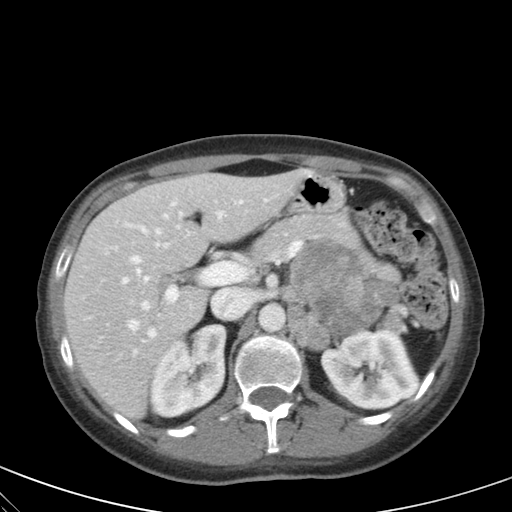
Contrast-enhanced abdominal CT, one axial slice. Position 35 of 59 along the scan axis. 120 kVp. Intravenous contrast given. Soft-tissue window (W 400 / L 40 HU). 4 mm slice thickness. 512 × 512 image matrix. Patient: female, 28 years. Case-level facts recorded for this patient, not image findings: diagnosis: adrenocortical carcinoma; tumour side: left adrenal; tumour size at pathology: 7 cm; Ki-67 index: 40 %; stage (as recorded): 4.
Outlined on this slice (semi-automatic segmentation, software-assisted and operator-edited):
- mass: bounding box (x1, y1, x2, y2) in pixels: (292, 240, 399, 341)